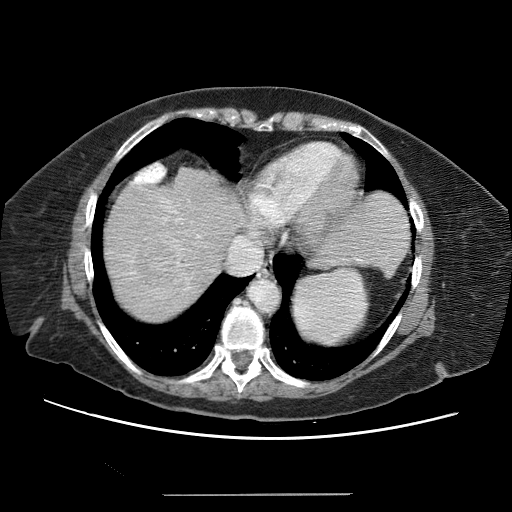
Contrast-enhanced abdominal CT (liver protocol), one axial slice. Slice 54 of 65 in the series (ordered by position). Reconstruction kernel STANDARD. Soft-tissue window (W 400 / L 40 HU). 2.5 mm slice thickness. 512 × 512 image matrix. Case-level facts recorded for this patient, not image findings: diagnosis: hepatocellular carcinoma (patient treated with transarterial chemoembolisation; whether this scan precedes or follows treatment is not stated here); TNM stage (as recorded): Stage-IIIB; Child-Pugh class: A; tumour differentiation: moderately differentiated.
Structures marked on this image (semi-automatic segmentation, software-assisted and operator-edited):
- abdominal aorta: bounding box (x1, y1, x2, y2) in pixels: (252, 281, 282, 312)
- liver parenchyma outside the tumour (the mass and vessels are separate outlines, so this box may not span the whole liver): (104, 166, 228, 312)
- mass: (130, 240, 182, 292)
- liver vessels: (115, 189, 209, 294)